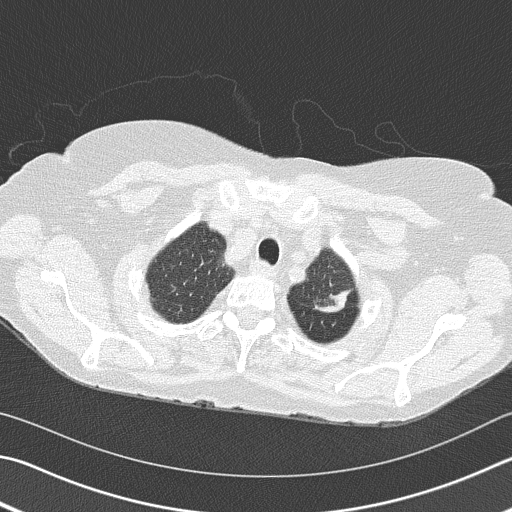
Axial slice from a low-dose chest CT screening exam, second annual screen, lung window (W 1500 / L -600 HU), 2 mm slice thickness, lung (sharp) reconstruction kernel (B50f), slice 136 of 153 in the series, 512 × 512 image matrix. Female, age 68 years at enrolment.
Expert-annotated lung lesion, box from (x=289, y=250) to (x=367, y=331) px. The exam's reader record, not a measurement of the box and not confirmed to be the same lesion: non-calcified nodule or mass ≥4 mm, left upper lobe, 4 × 2 mm, spiculated (stellate) margins, soft tissue attenuation, pre-existing on the prior screen: yes; interval growth: yes. Lung cancer was diagnosed 392 days after this screen (after the third annual screen): adenocarcinoma, NOS, left upper lobe, poorly differentiated (G3), stage IB (AJCC 6th edition), 50 mm at pathology.